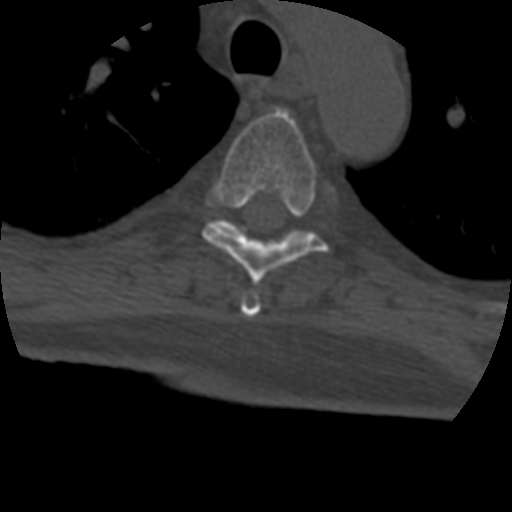
CT including the spine, one axial slice; position 318 of 399 along the scan axis; 120 kVp; bone window (W 1800 / L 400 HU); 512 × 512 image matrix. Patient age 69 years. From the clinical record (not read from this slice): primary cancer: prostate.
Structures marked on this image (semi-automatic segmentation, software-assisted and operator-edited):
- T4 vertebra: bounding box <241,291,261,318> (left, top, right, bottom; pixels)
- T5 vertebra: <202,110,330,285>
- T6 vertebra: <224,223,306,234>